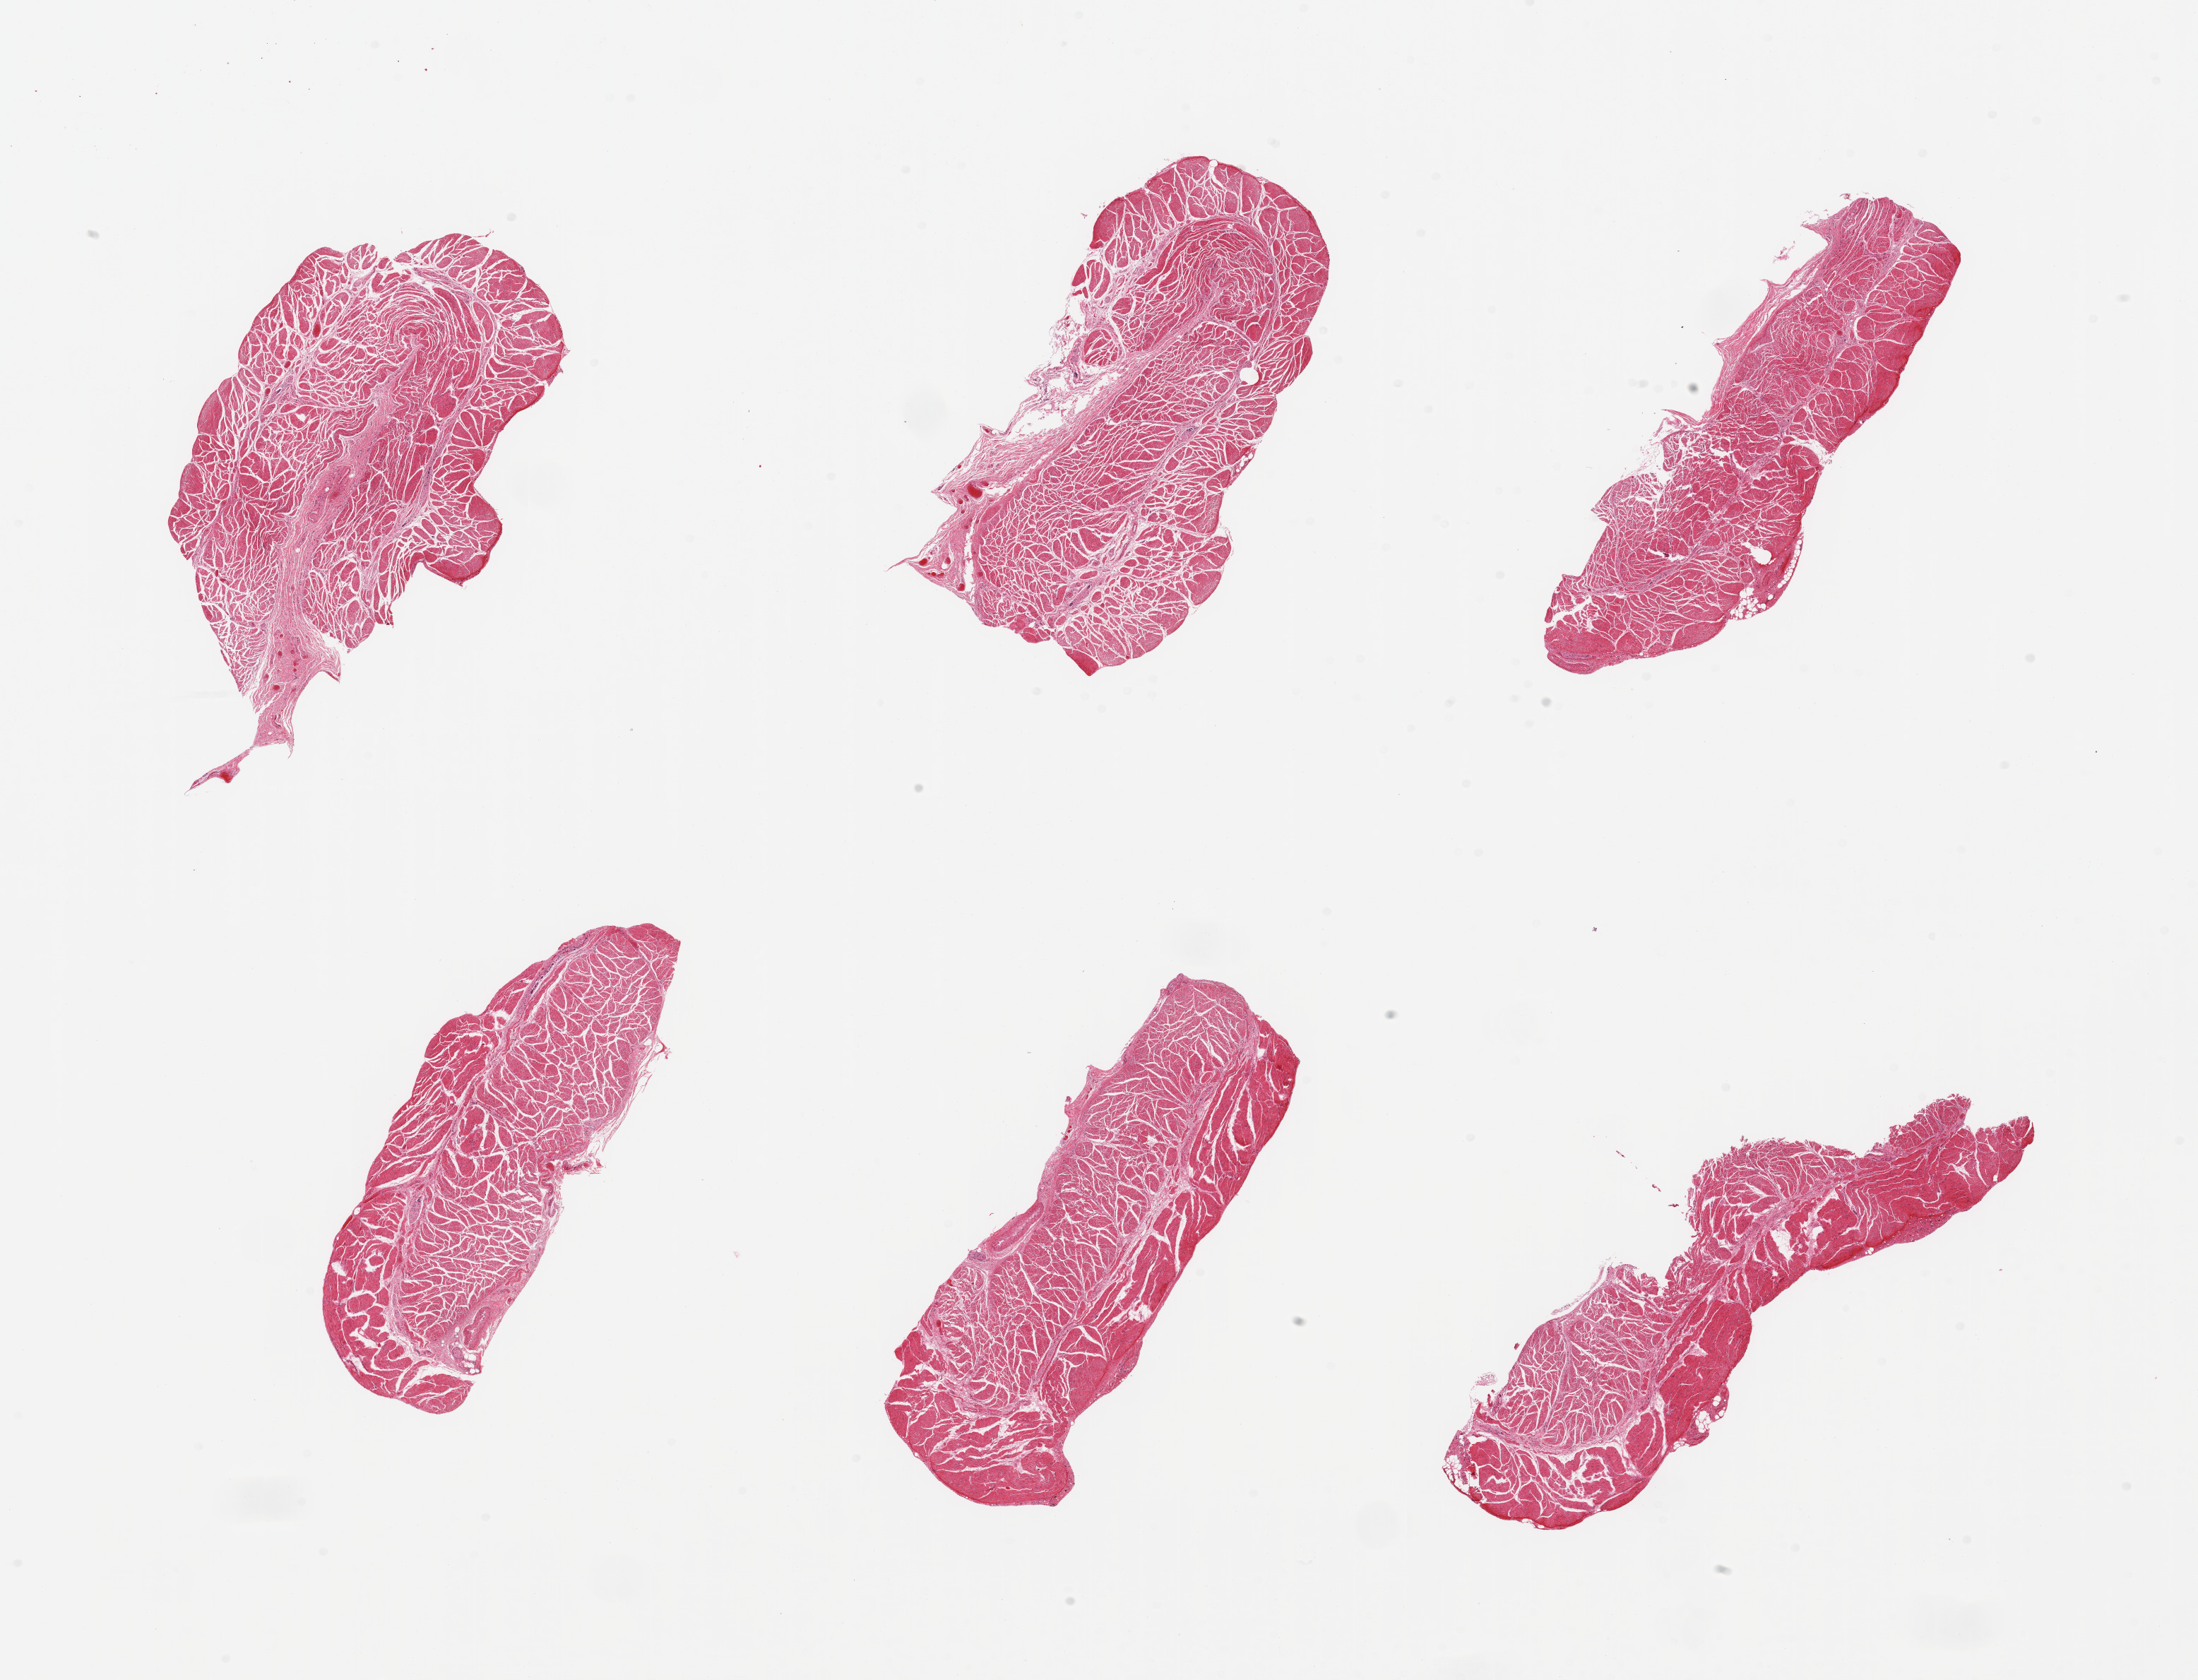
H&E whole-slide image, low-resolution overview of the scanned area, about 24.6 x 18.8 mm (acquisition: 20x scan), PAXgene-fixed paraffin-embedded (PFPE) section, target tissue: esophageal muscle, donor tissue sample. Male donor.
Review note (as recorded): 6 pieces; well trimmed target muscularis.